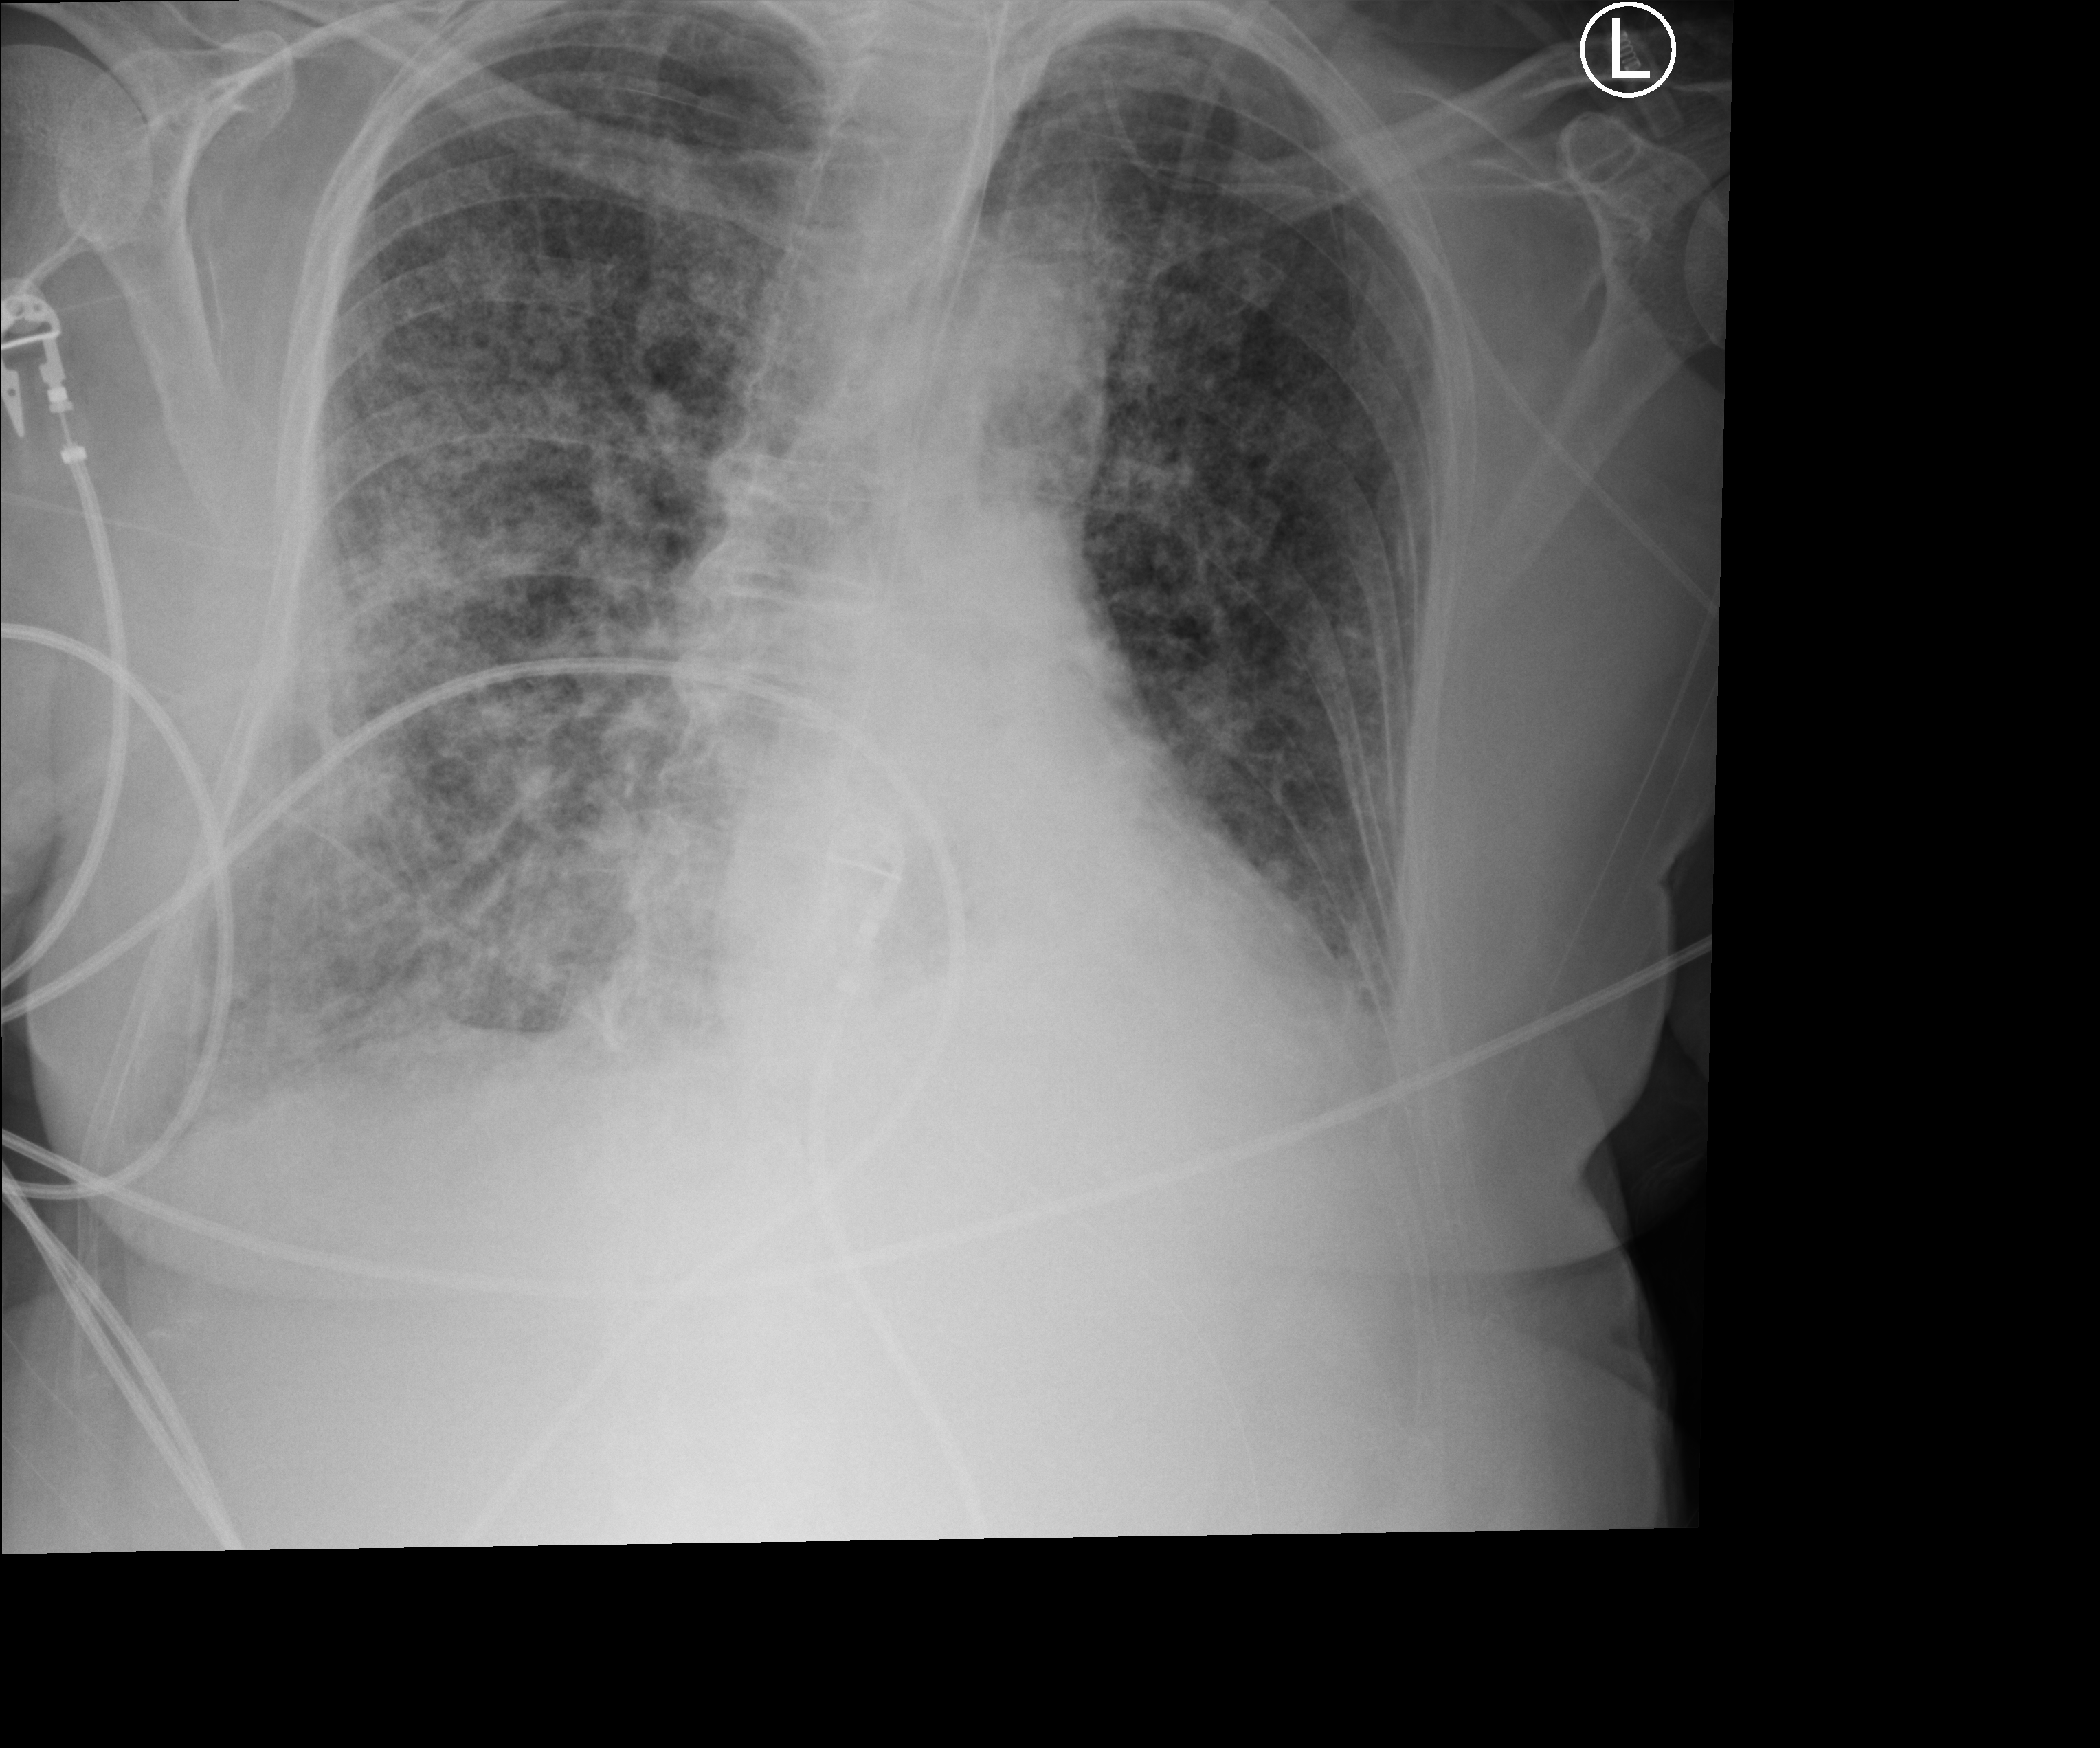
Chest X-ray (portable); anteroposterior (AP) projection. Patient hospitalised with COVID-19; female, aged 75–90 years.
From the hospital-stay record, not from the radiograph (when in the stay this image was taken is not recorded): COPD (admission record): no; other chronic lung disease (admission record): yes; length of hospital stay: 70 days.